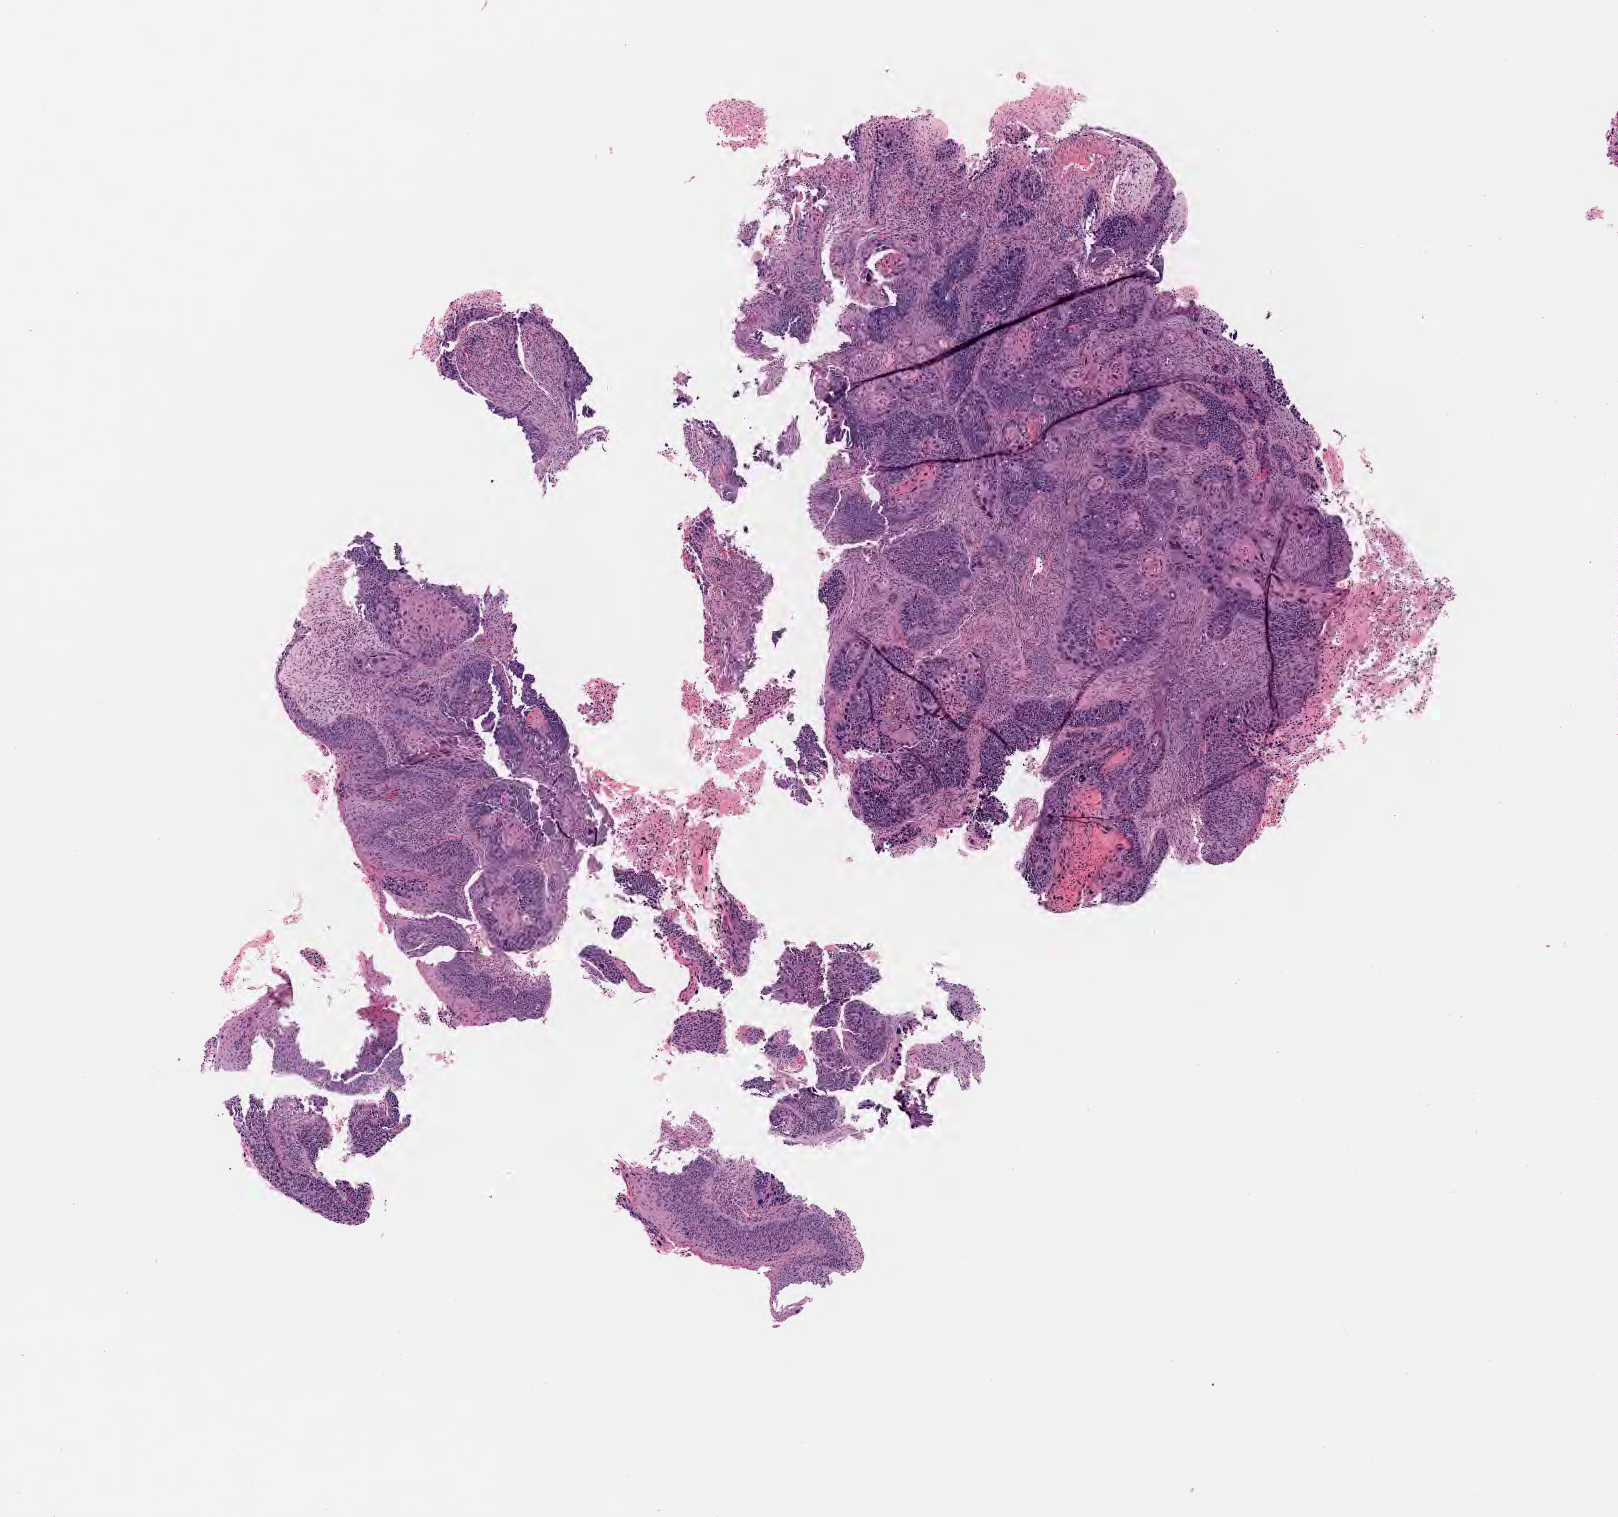
Digitized hematoxylin and eosin (H&E)-stained section — shown as a low-resolution overview of the whole scanned area (about 6.5 x 6.1 mm), tumor tissue, anatomic site: cervix. Female patient, 59 years old.
Histologic diagnosis: Squamous cell carcinoma, keratinizing, NOS.